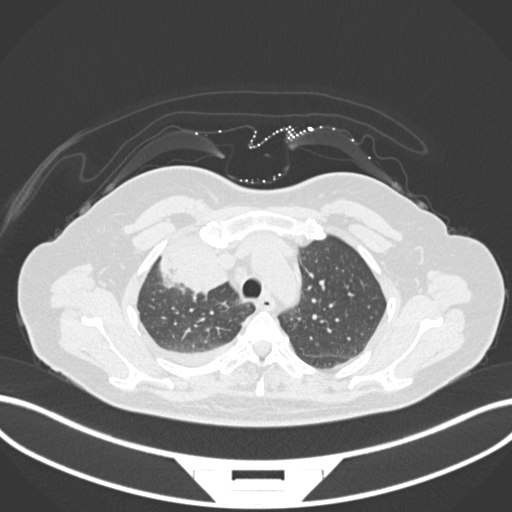
Chest CT, one axial slice; position 126 of 172 along the scan axis; 120 kVp; lung window (W 1500 / L -600 HU); 1 mm slice thickness; 512 × 512 image matrix, field of view 400 × 400 mm. Female patient, age 52 years. From the clinical record (not read from this slice): clinical TNM (as recorded): T3 N1 M1.
Outlined on this slice (rectangle marked by the reading radiologist):
- lung tumour (recorded histology: adenocarcinoma): bounding box (x1, y1, x2, y2) in pixels: (155, 236, 234, 289)